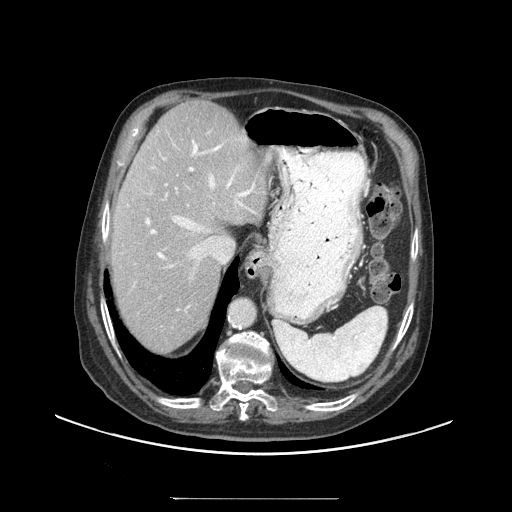
Contrast-enhanced abdominal CT (liver protocol), one axial slice; slice 74 of 97 in the series (ordered by position); reconstruction kernel STANDARD; soft-tissue window (W 400 / L 40 HU); 2.5 mm slice thickness; 512 × 512 image matrix, field of view 450 × 450 mm. From the clinical record (not read from this slice): diagnosis: hepatocellular carcinoma (patient treated with transarterial chemoembolisation; whether this scan precedes or follows treatment is not stated here); TNM stage (as recorded): Stage-IIIC; Child-Pugh class: A; tumour differentiation: well differentiated; tumour nodularity: uninodular.
Structures marked on this image (semi-automatic segmentation, software-assisted and operator-edited):
- abdominal aorta: bounding box <230,299,256,327> (left, top, right, bottom; pixels)
- liver parenchyma outside the tumour (the mass and vessels are separate outlines, so this box may not span the whole liver): <110,100,266,352>
- liver vessels: <145,131,255,311>